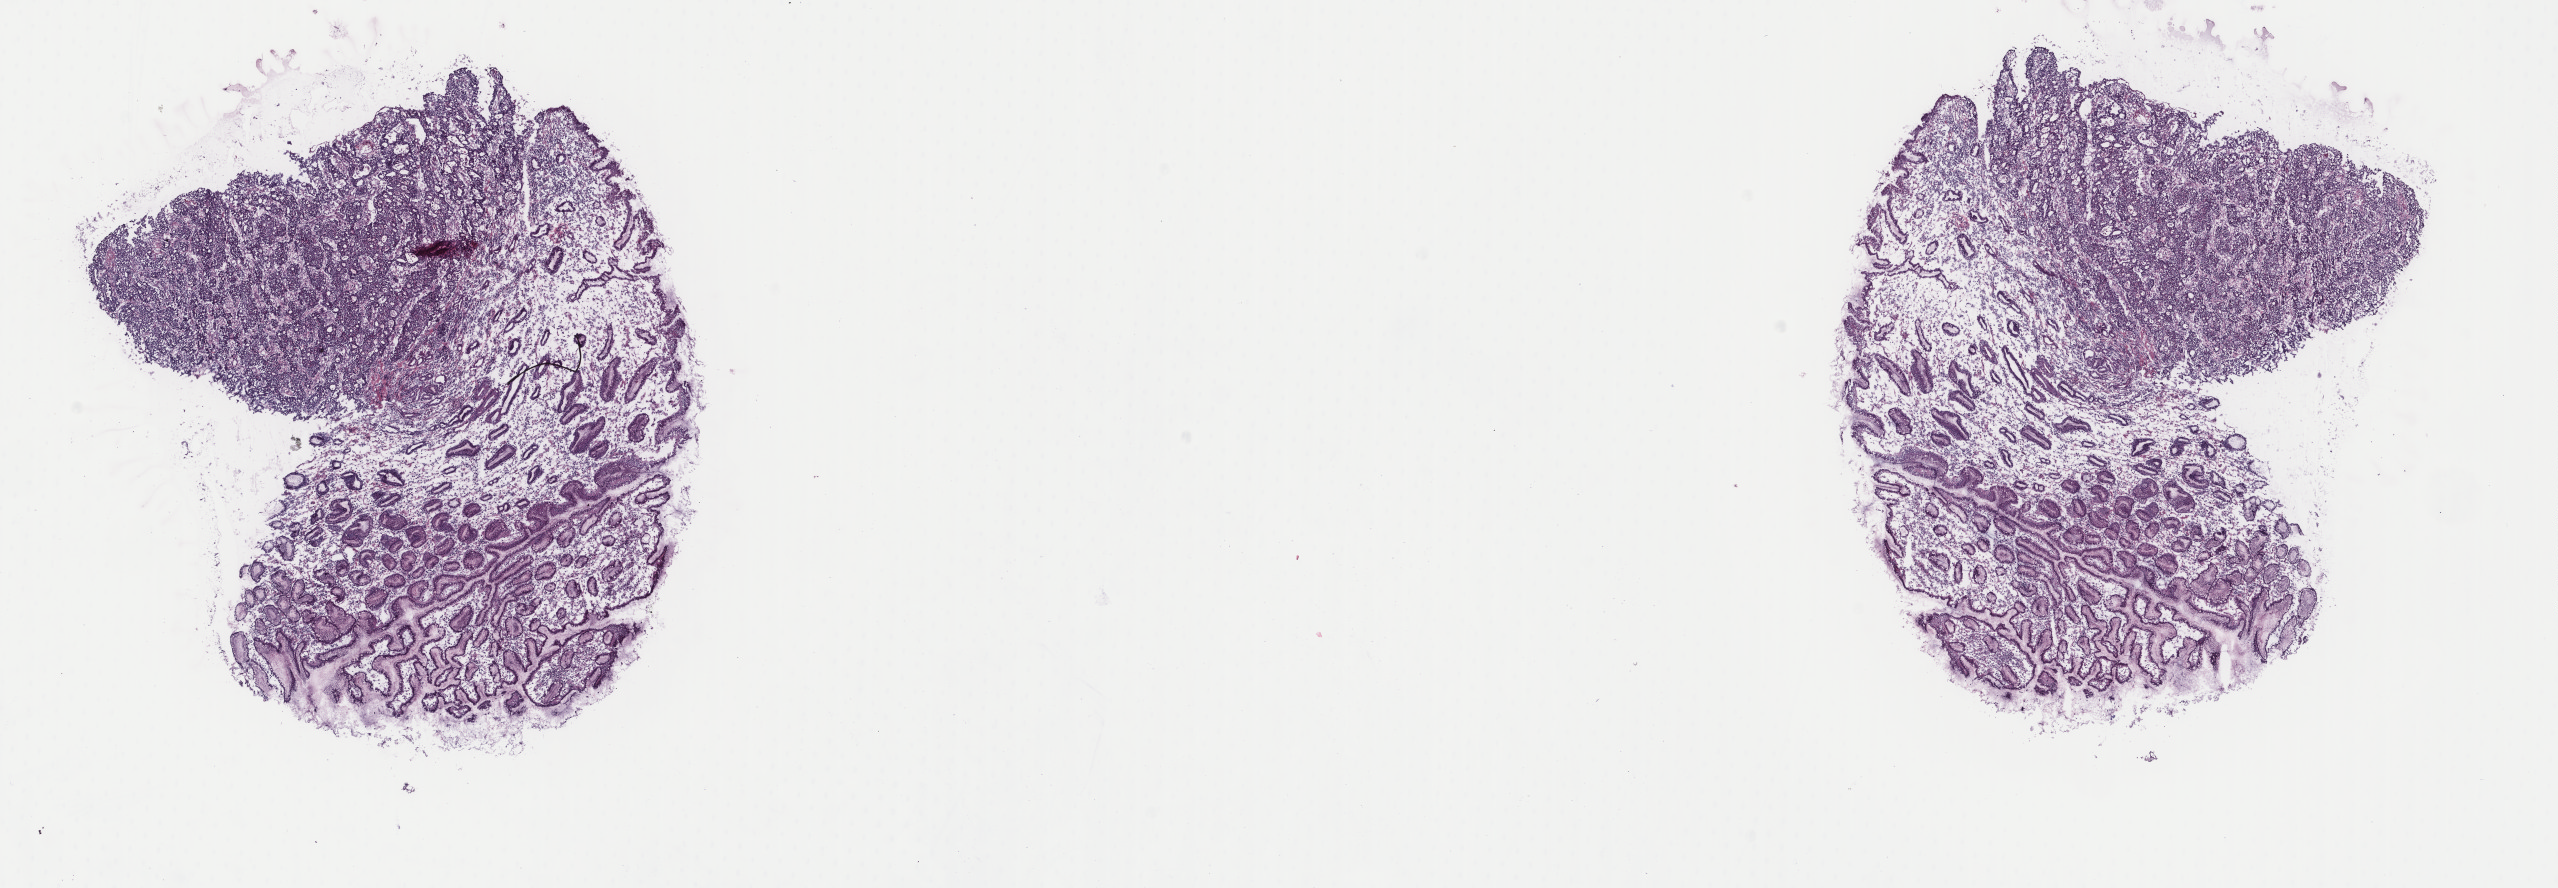
Digitized H&E tissue section (whole slide), shown as a low-resolution overview of the whole scanned area (about 20.3 x 7.0 mm). Frozen section from the top of the tissue portion. Stomach, primary tumour sample. Female patient; age at initial diagnosis 71 years. Histologic grade: G3 (poorly differentiated). Pathologist review of this section (percent, as recorded): tumour cells 65%, tumour nuclei 65%, normal cells 15%, stromal cells 20%, necrosis 0%. Infiltration values recorded for this section: lymphocyte infiltration 5%, monocyte infiltration 1%, neutrophil infiltration 2%.
Lymph nodes positive (case pathology): 1 of 64 examined. Pathologic diagnosis: Carcinoma, diffuse type (gastric antrum). AJCC pathologic stage: IIB (7th edition). TNM: T3 N1 M0.